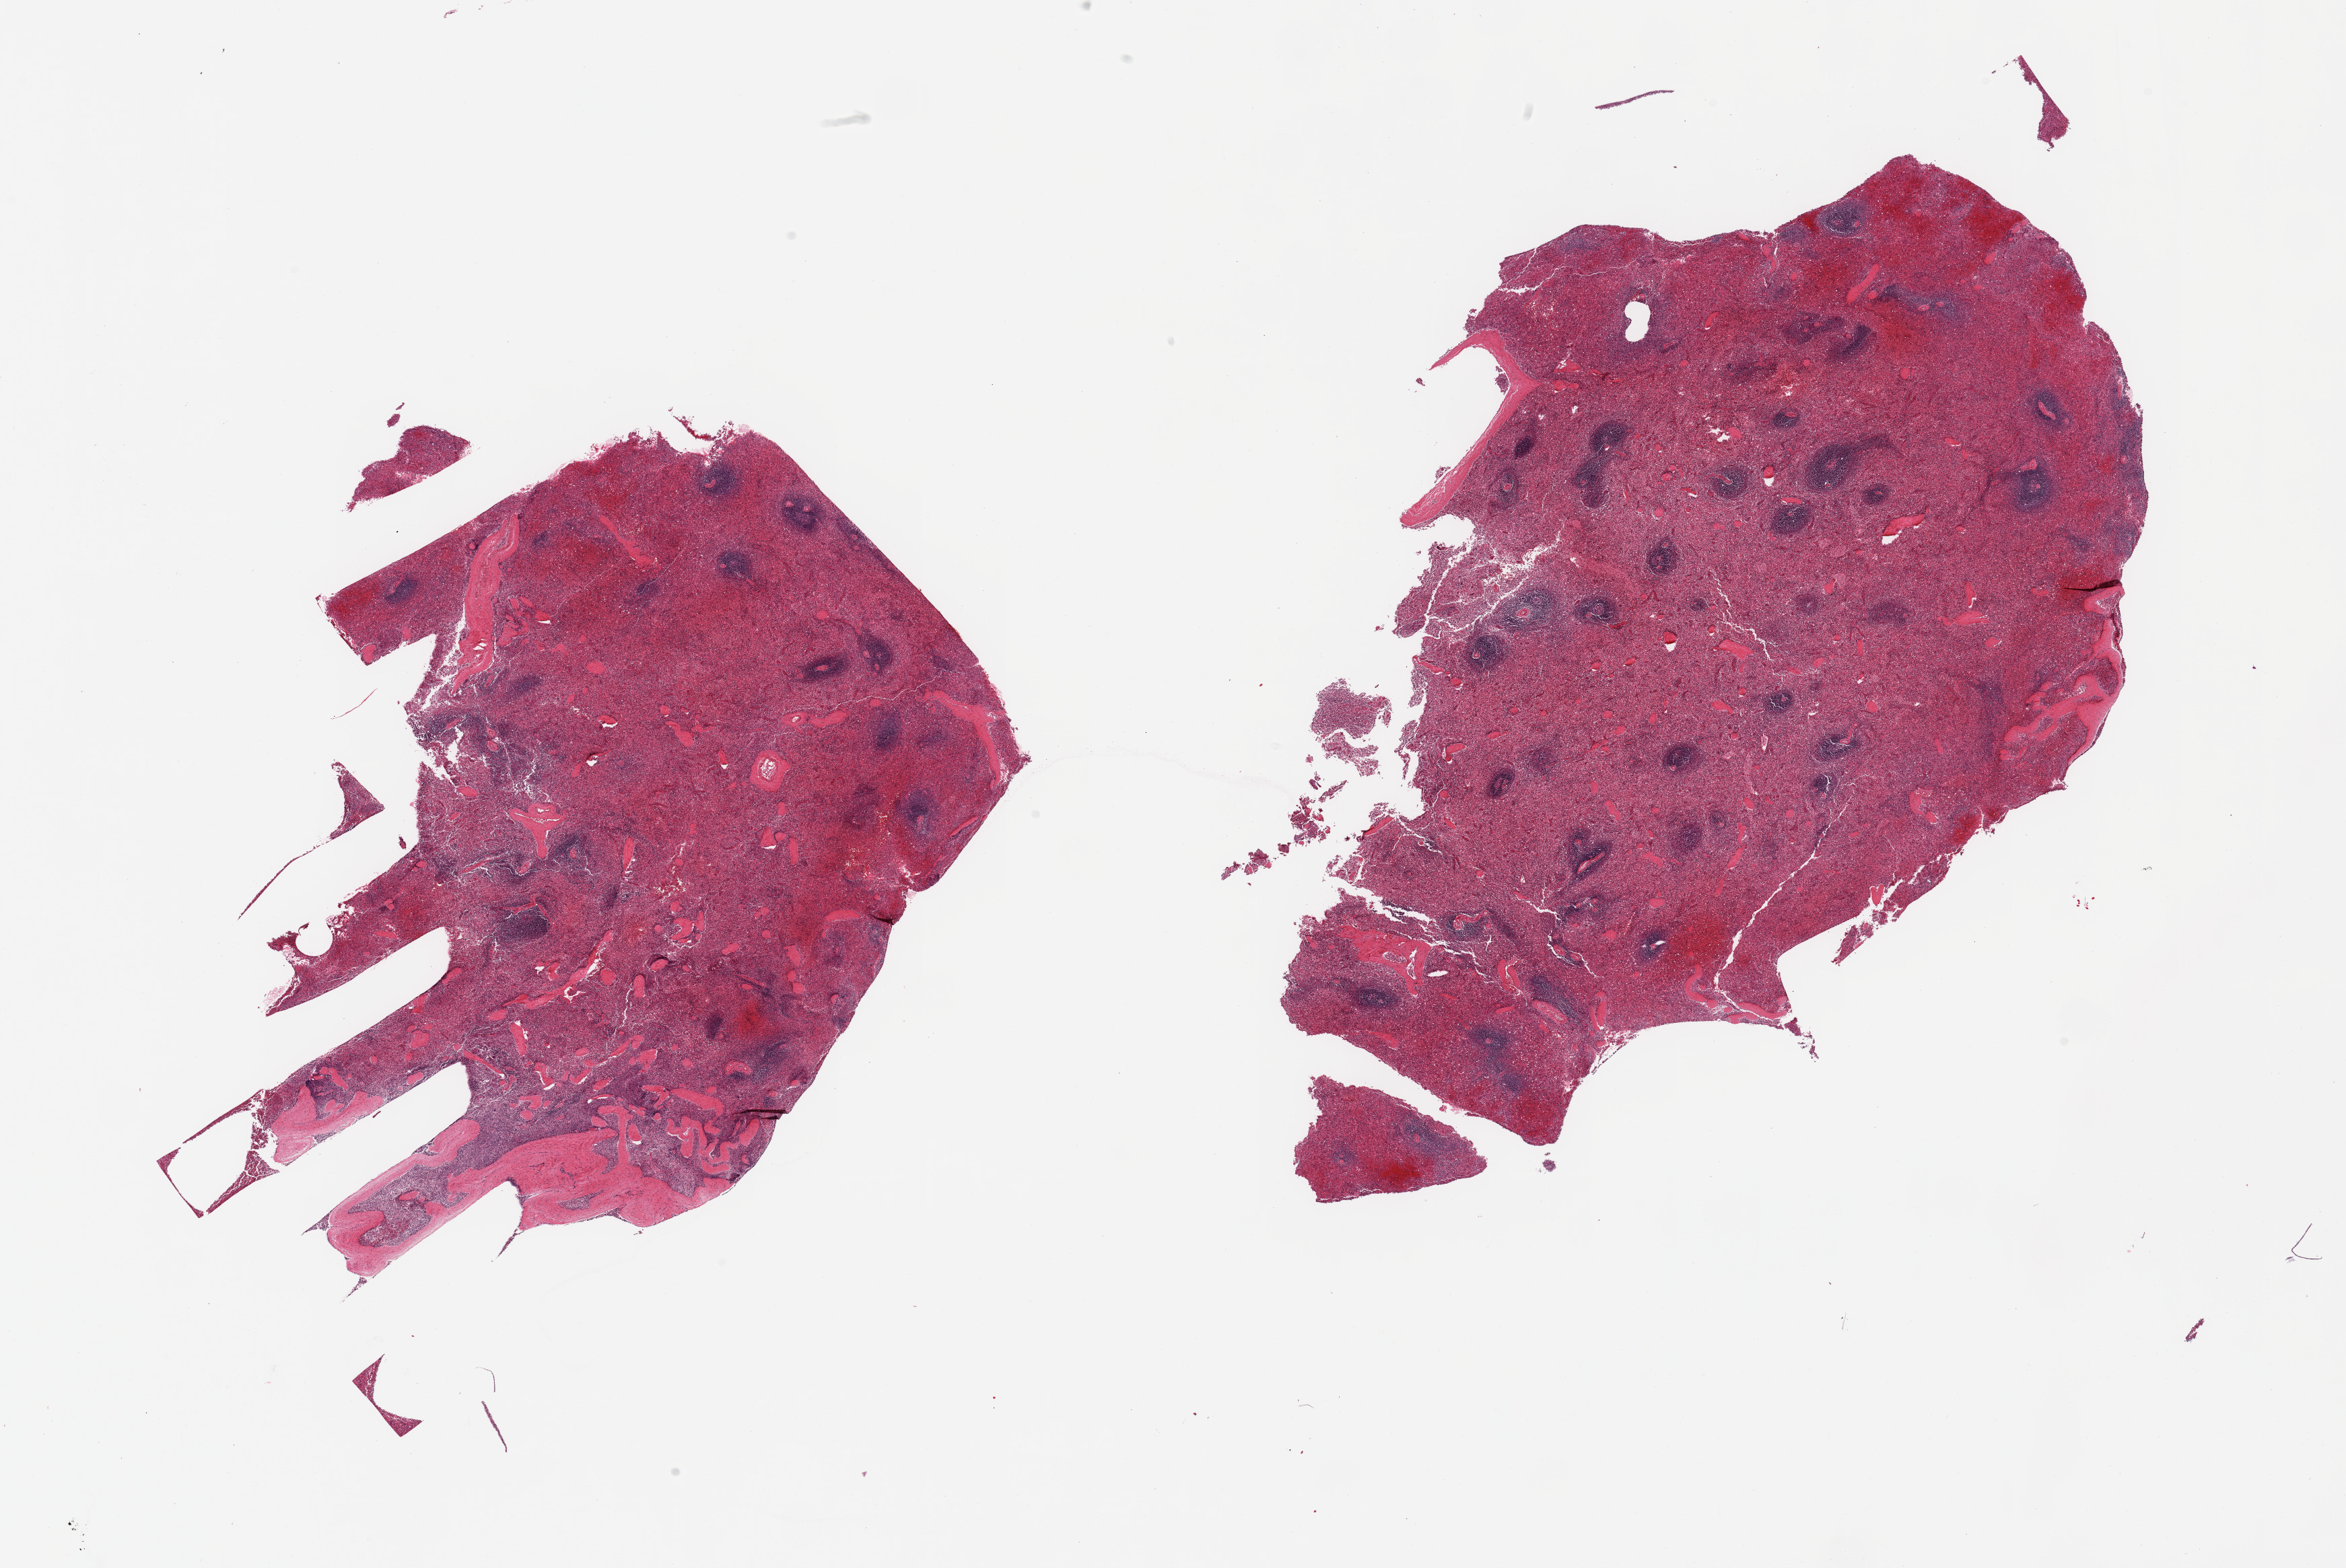
H&E whole-slide image, whole scanned area (about 27.6 x 18.4 mm, slide scanned at 20x) shown as a low-resolution overview. PAXgene-fixed, paraffin-embedded tissue. Sampled site (target tissue): spleen. Donor tissue sample. Donor: female.
Pathologist's review note for this sample: 2 pieces.